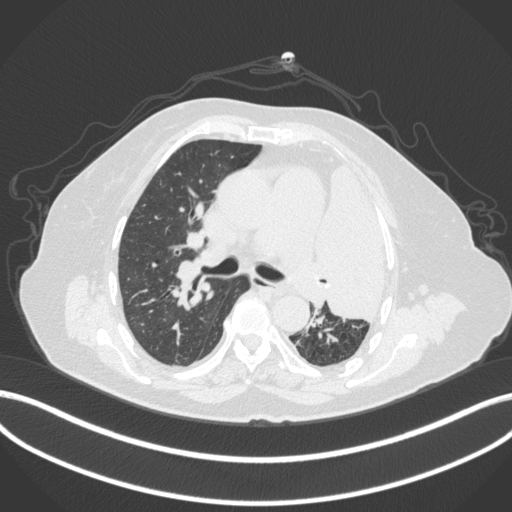
Chest CT, one axial slice. 120 kVp. Lung window (W 1500 / L -600 HU). 1 mm slice thickness. 512 × 512 image matrix, field of view 400 × 400 mm. Female patient, age 75 years. Case-level facts recorded for this patient, not image findings: clinical TNM (as recorded): T3 N3 M1.
Annotated regions visible in this slice (rectangle marked by the reading radiologist):
- lung tumour (recorded histology: adenocarcinoma): box from (x=317, y=156) to (x=398, y=328) px